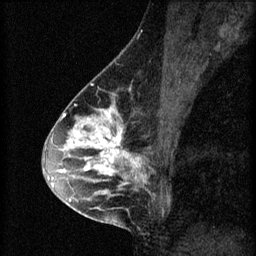
Breast MRI (dynamic contrast-enhanced), one sagittal slice; position 34 of 60 along the scan axis; 3 images stored at this slice position (order not interpretable as contrast timing); 1.5 T; TE 4.2 ms, TR 8.2 ms; 256 × 256 image matrix. Patient: female, 45 years.
Outlined on this slice (semi-automatic segmentation, software-assisted and operator-edited):
- analysis volume of interest (the breast-tissue region the enhancement analysis was run in; not a lesion): bounding box (x1, y1, x2, y2) in pixels: (54, 104, 155, 217)
- tumour enhancement mask (voxels above the 70 % enhancement threshold inside the analysis volume of interest): (54, 104, 147, 207)